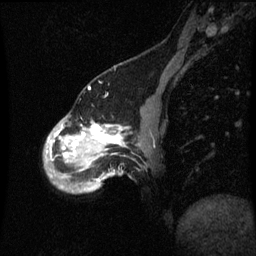
Breast MRI (dynamic contrast-enhanced), one sagittal slice. Position 15 of 60 along the scan axis. Dynamic contrast-enhanced series, image 2 of 3 at this slice position (ordered by acquisition). 1.5 T. TE 4.2 ms, TR 8.9 ms. 2 mm slice thickness. 256 × 256 image matrix, field of view 200 × 200 mm. Female patient, age 49 years. Case-level facts recorded for this patient, not image findings: setting: breast cancer imaged before/during neoadjuvant chemotherapy; receptor status: HR-positive, HER2-negative.
Annotated regions visible in this slice (semi-automatic segmentation, software-assisted and operator-edited):
- analysis volume of interest (the breast-tissue region the enhancement analysis was run in; not a lesion): bounding box [x1, y1, x2, y2] px = [44, 114, 143, 193]
- tumour enhancement mask (voxels above the 70 % enhancement threshold inside the analysis volume of interest): [48, 124, 123, 157]